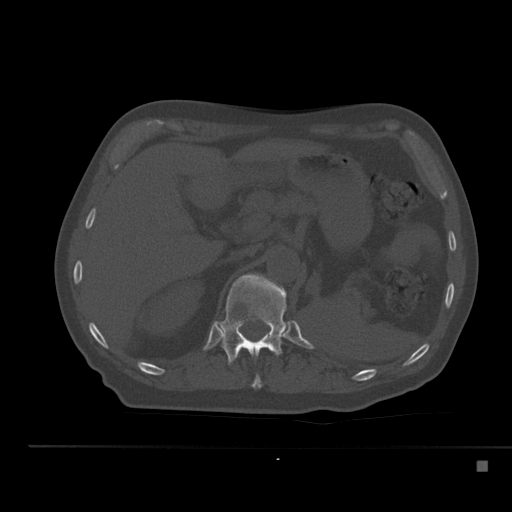
CT including the spine, one axial slice; slice 230 of 517 in the series (ordered by position); reconstruction kernel Br40s; bone window (W 1800 / L 400 HU); 512 × 512 image matrix, field of view 408 × 408 mm. Male patient, age 70 years. From the clinical record (not read from this slice): primary cancer: renal.
Outlined on this slice (semi-automatically segmented with operator editing):
- T11 vertebra: bounding box <251,374,262,389> (left, top, right, bottom; pixels)
- T12 vertebra: <215,274,289,365>